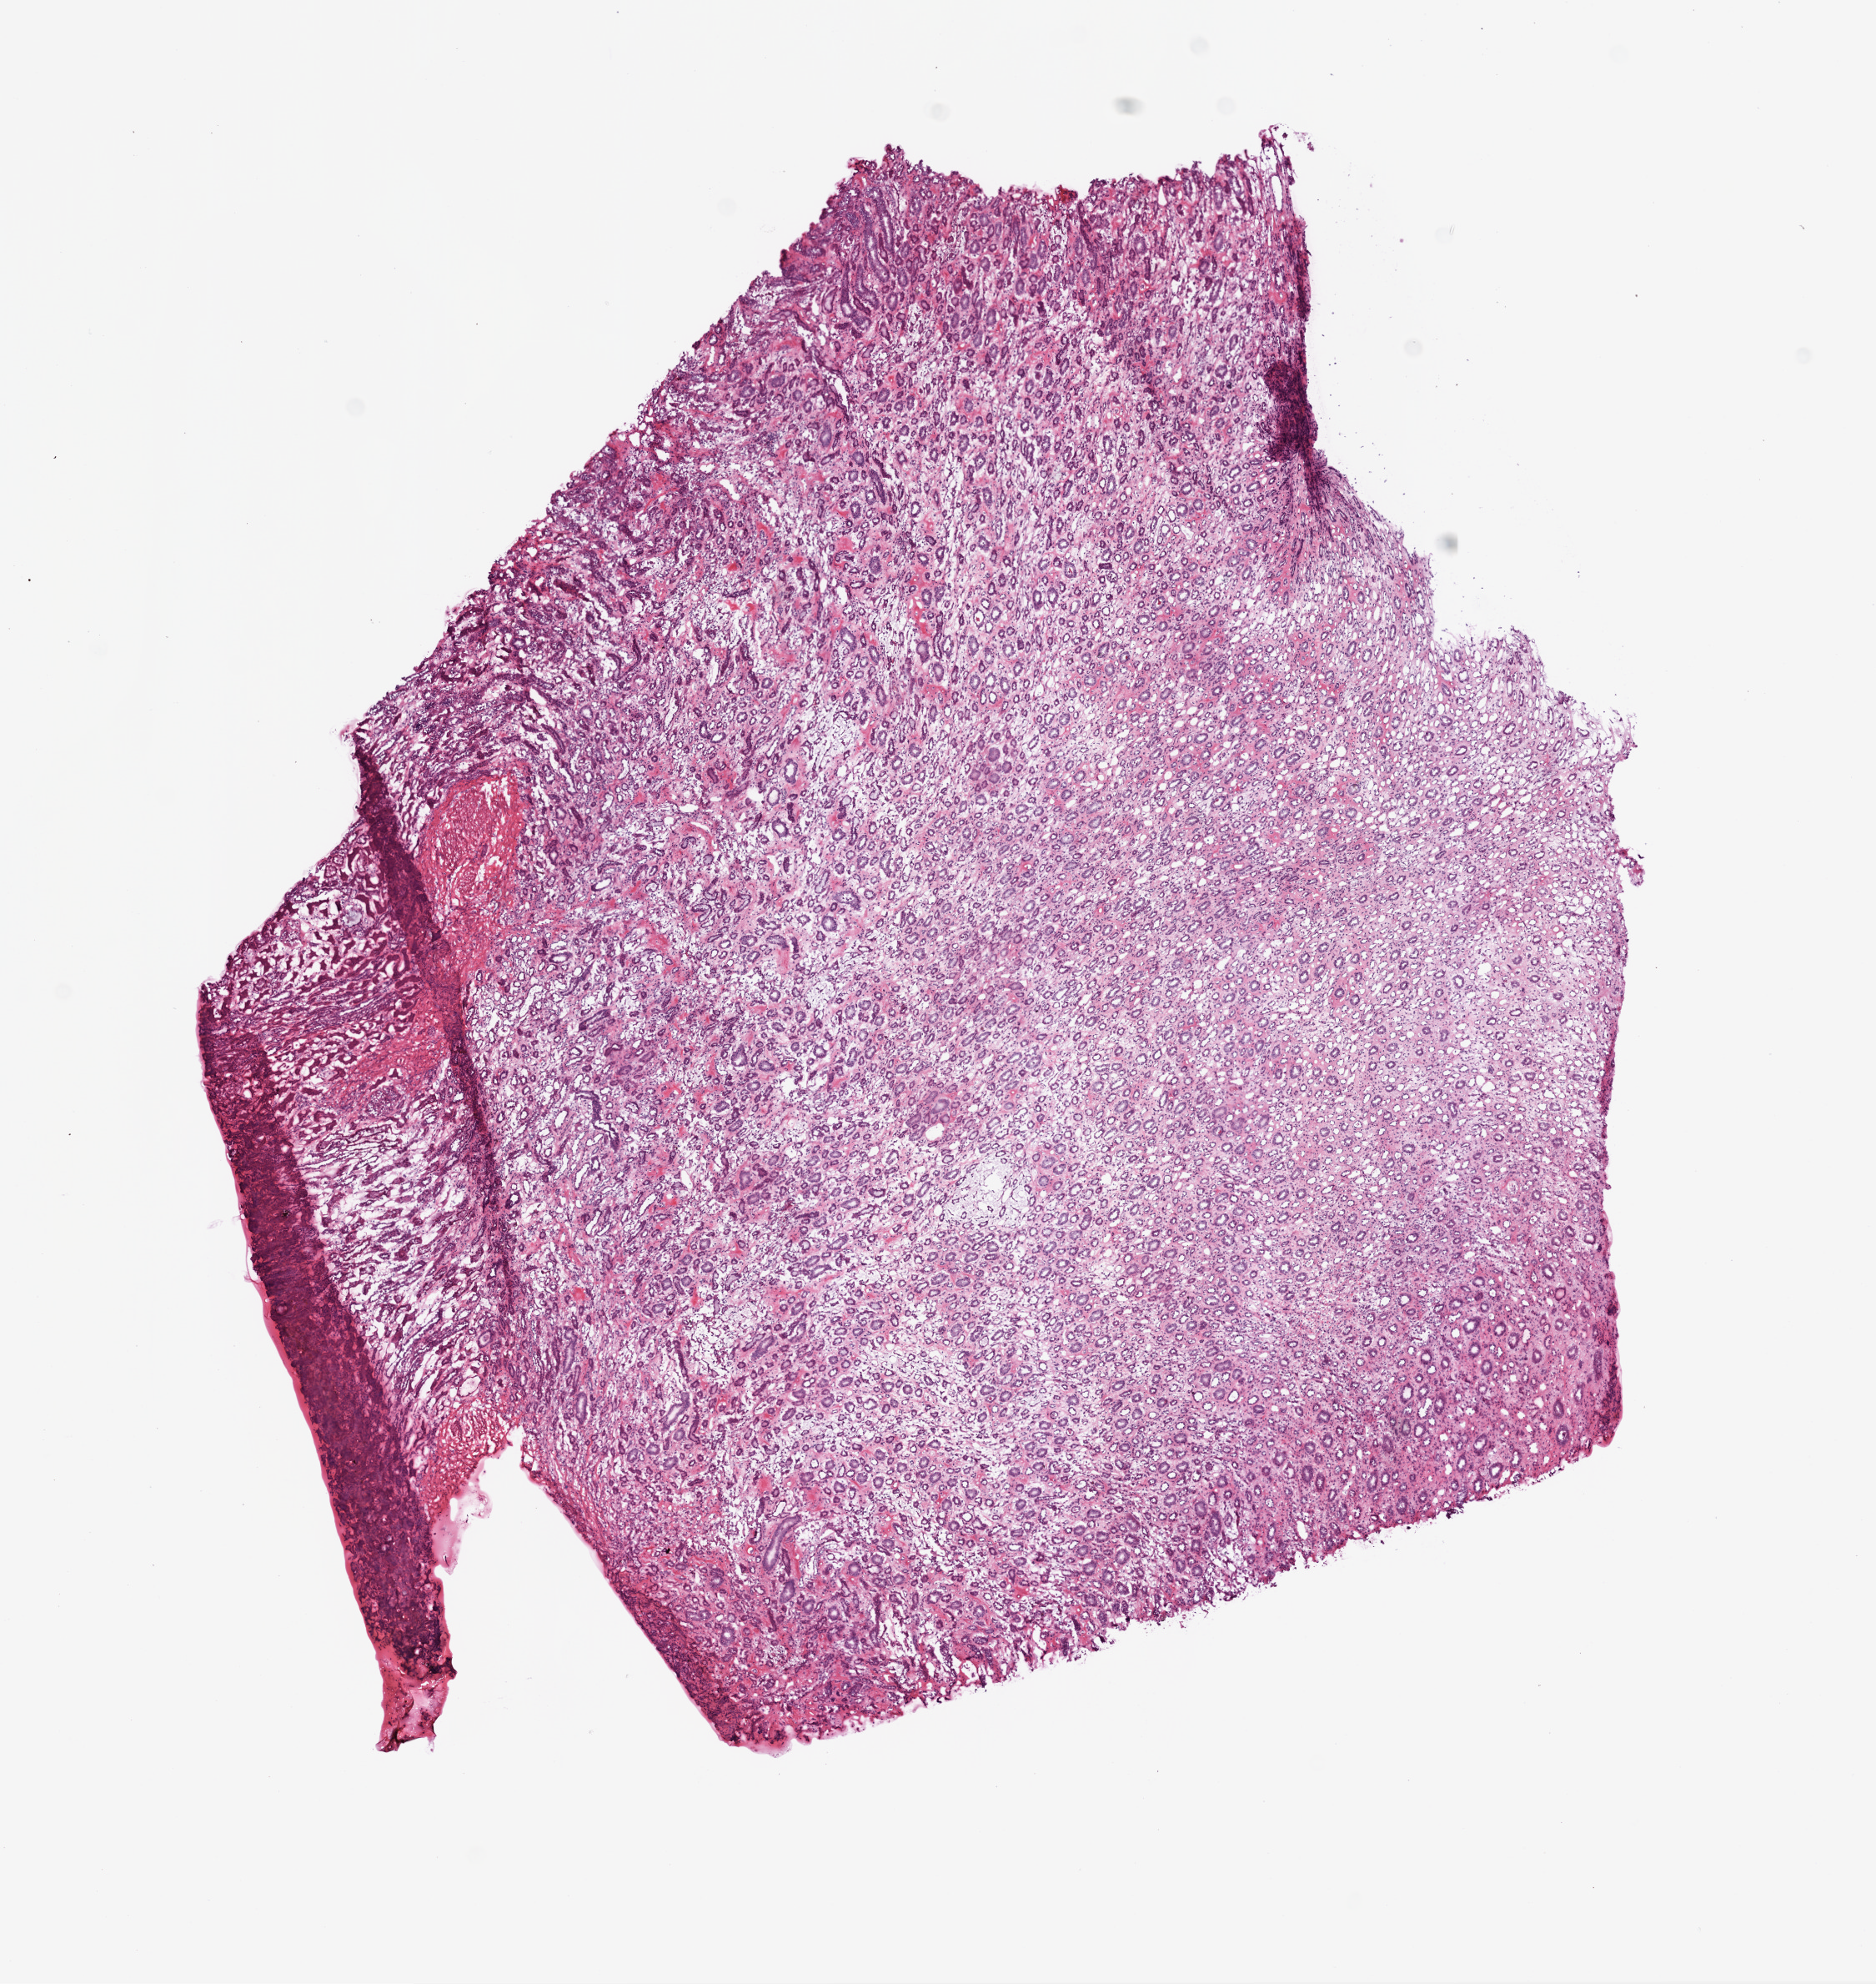
Whole-slide histology image, Hematoxylin and eosin (H&E) stained, a low-resolution overview of the entire scanned area, about 9.0 x 9.5 mm (from a 20x scan); frozen section from the top of the tissue portion; sample: solid tissue normal (non-tumour tissue), kidney. Female patient; age at initial diagnosis 51 years.
This section: solid tissue normal (non-tumour) sample from the same patient. Patient diagnosis: Clear cell adenocarcinoma, NOS.